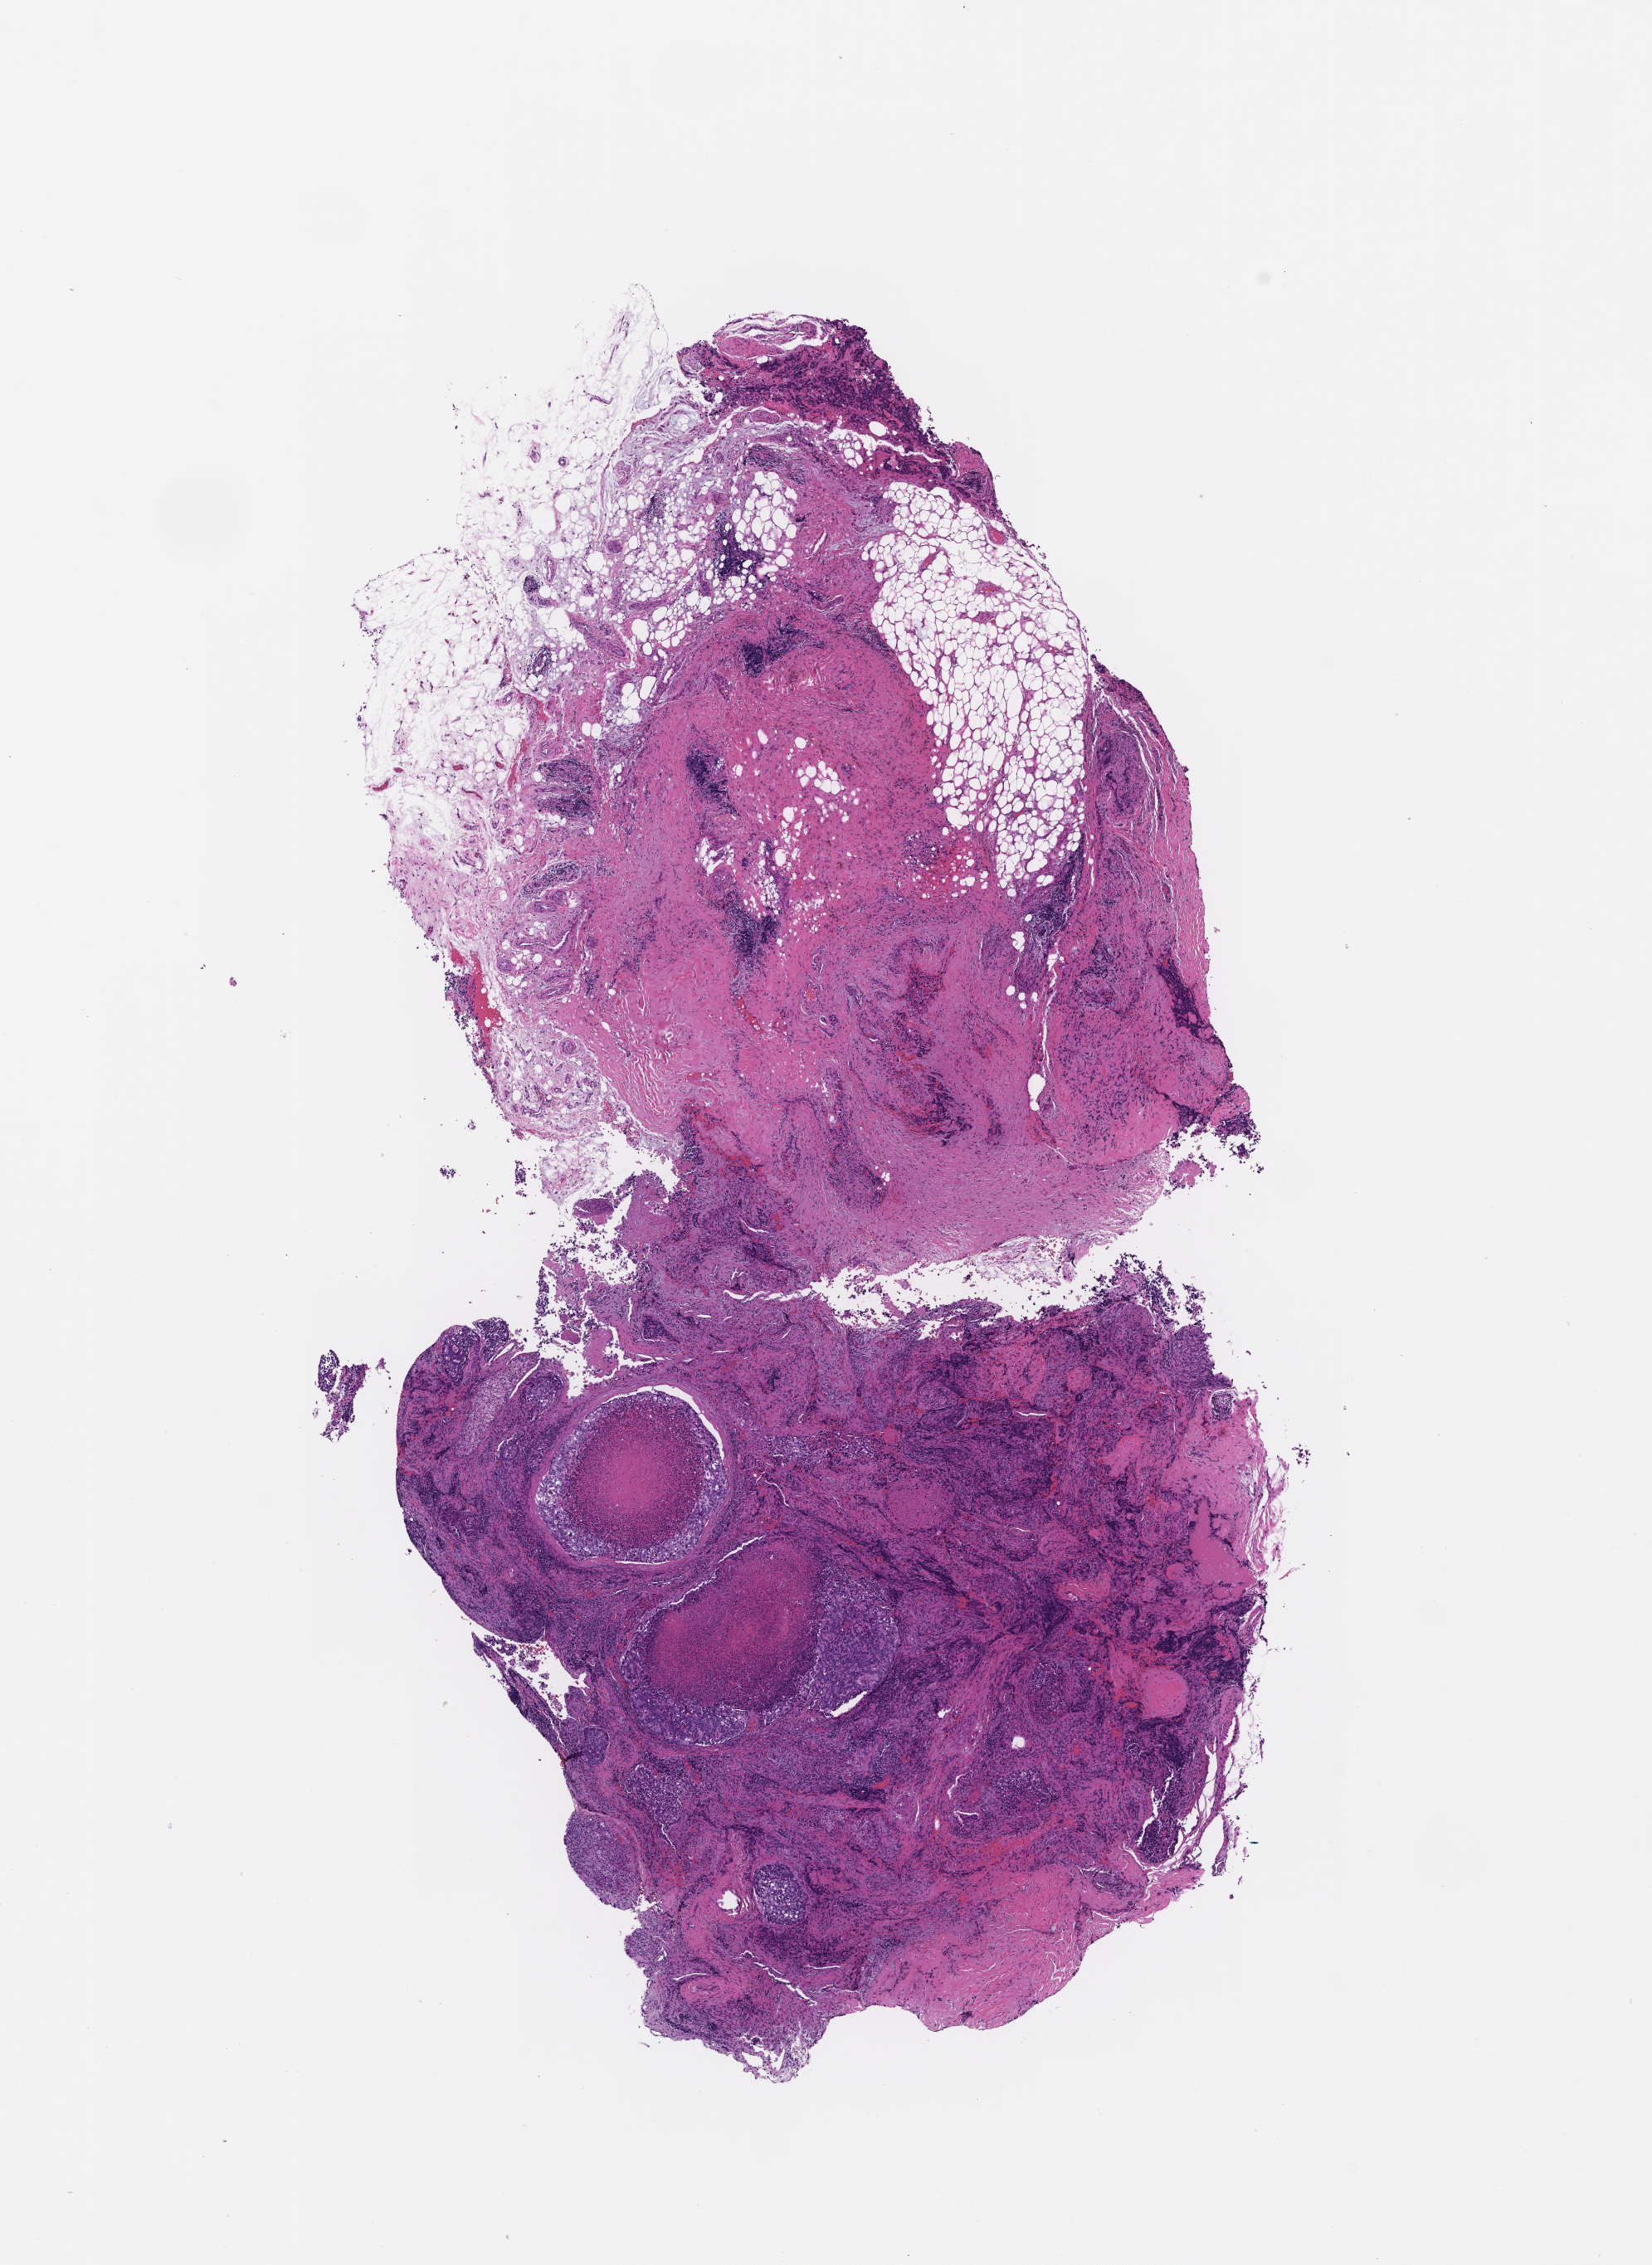
Whole-slide image, H&E stain — whole scanned area (about 8.0 x 11.0 mm) shown as a low-resolution overview; FFPE section. Patient sex: male.
This section: metastasis (sampled organ not recorded). Patient diagnosis (primary): Non-Small Cell Lung Carcinoma.